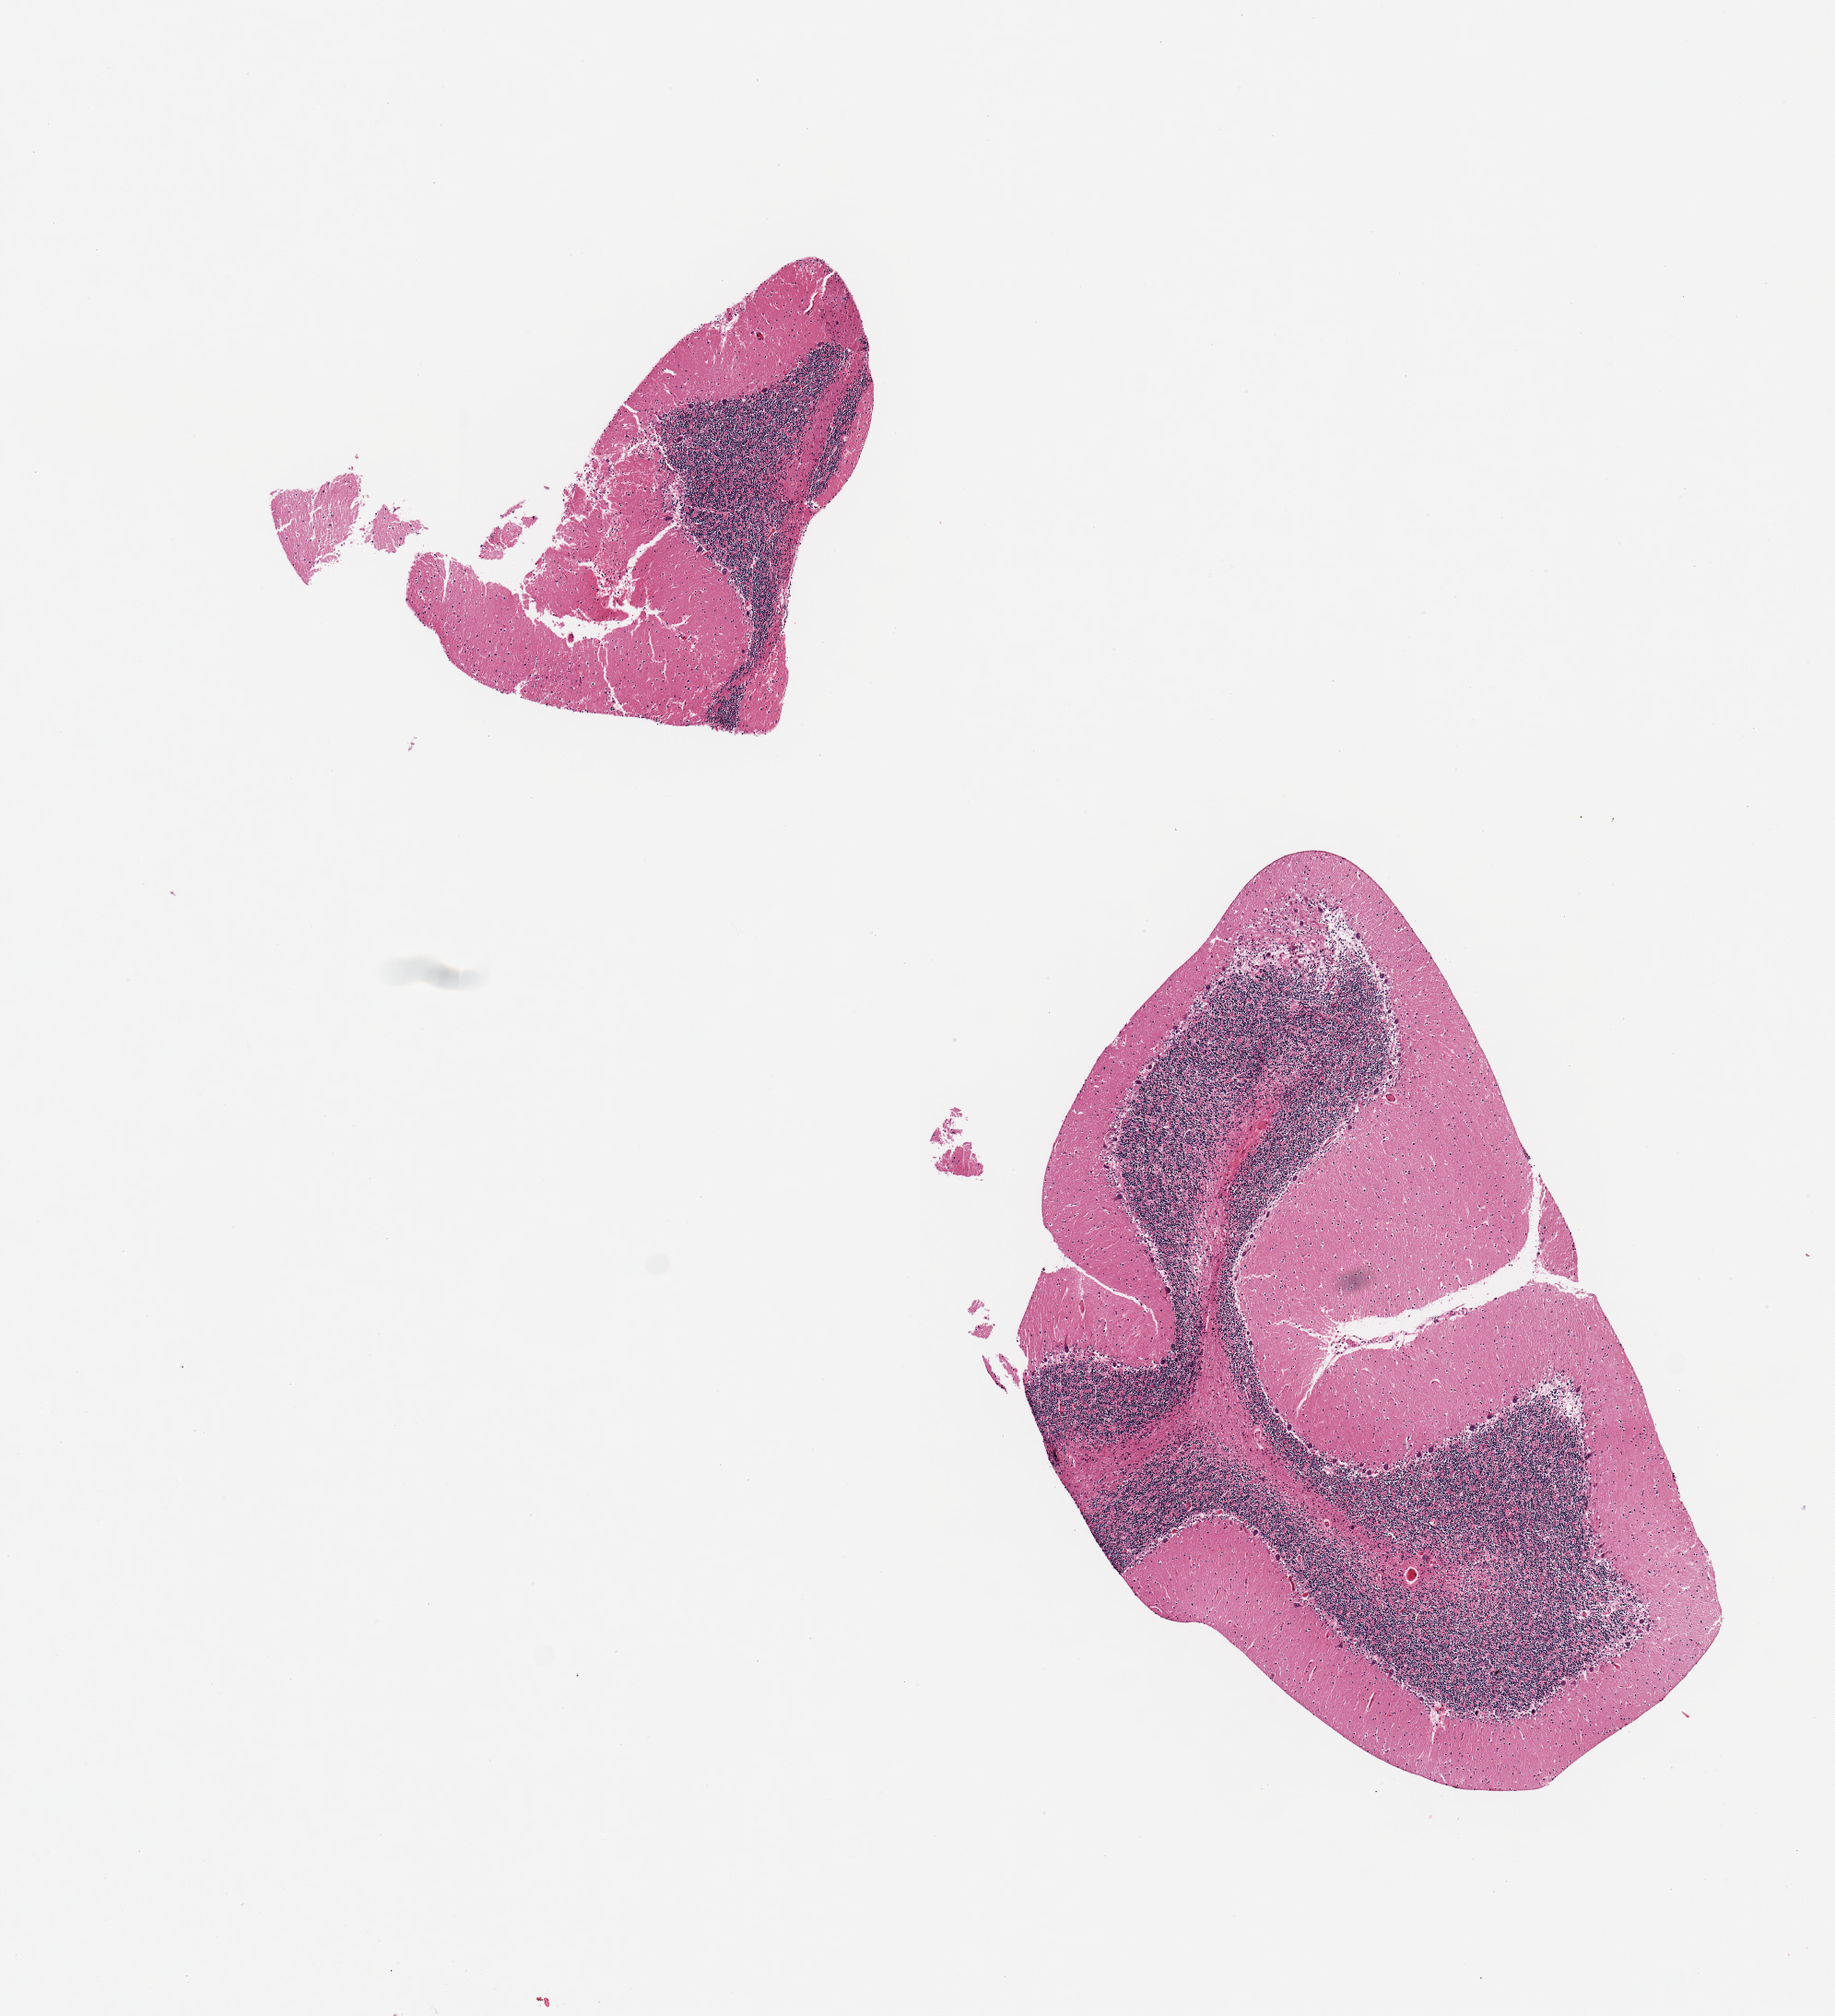
Hematoxylin and eosin (H&E) whole-slide image — a low-resolution overview of the entire scanned area, about 7.9 x 8.7 mm (acquisition: 20x scan). PAXgene-fixed, paraffin-embedded tissue. Target tissue: pituitary. Donor tissue sample. Female donor.
Reviewer comment on this tissue sample: 2 pieces of cerebellum.